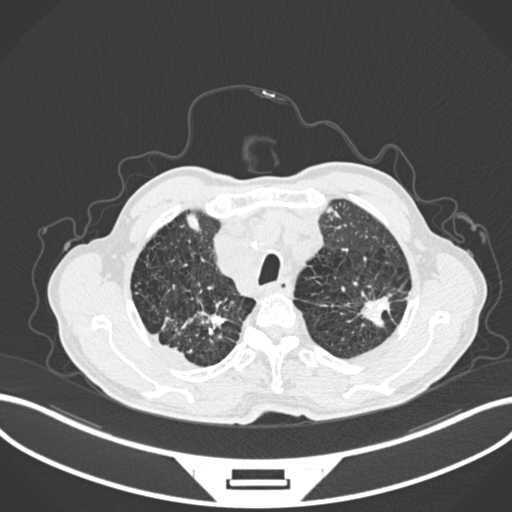
Chest CT, one axial slice. Position 230 of 287 along the scan axis. Lung window (W 1500 / L -600 HU). 1 mm slice thickness. 512 × 512 image matrix, field of view 400 × 400 mm. Patient: male, 74 years. Case-level facts recorded for this patient, not image findings: clinical TNM (as recorded): T2a N1 M0.
Outlined on this slice (bounding box drawn by a radiologist):
- lung tumour (recorded histology: adenocarcinoma): bounding box [x1, y1, x2, y2] px = [359, 290, 396, 331]